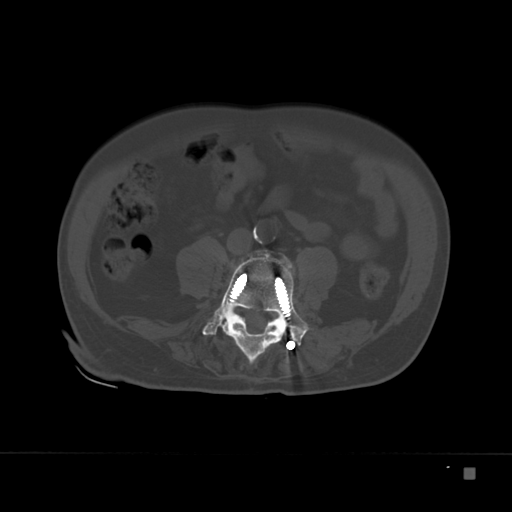
CT including the spine, one axial slice. Slice 45 of 332 in the series (ordered by position). 120 kVp. Bone window (W 1800 / L 400 HU). 1.5 mm slice thickness. 512 × 512 image matrix, field of view 389 × 389 mm. Patient: male, 72 years. From the clinical record (not read from this slice): primary cancer: skeletal.
Outlined on this slice (semi-automatically segmented with operator editing):
- L4 vertebra: bounding box <202,250,312,363> (left, top, right, bottom; pixels)